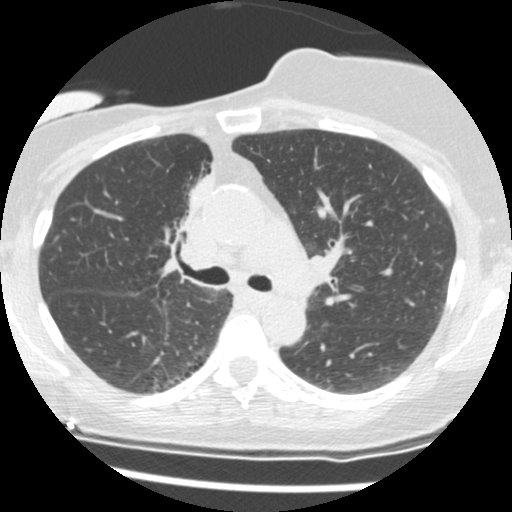
Low-dose screening chest CT, axial slice. Second annual screen. Lung window (W 1500 / L -600 HU). 2.5 mm slice thickness. Slice 50 of 165 in the series. 512 × 512 image matrix, field of view 296 × 296 mm. Female participant, aged 56 years at enrolment.
Expert-annotated lung lesion, bounding box (x1, y1, x2, y2) in pixels: (153, 172, 209, 262). The screening reader recorded 2 non-calcified nodules or masses ≥4 mm on this exam; which of them this box marks is not recorded. Official screen result: positive, change unspecified: nodule(s) >= 4 mm or enlarging nodule(s), mass(es), or other non-specific abnormalities suspicious for lung cancer. Later outcome: lung cancer diagnosed 675 days after this screen (after the third annual screen) — adenocarcinoma, NOS, right upper lobe, stage IIIB (AJCC 6th edition), 8 mm at pathology.